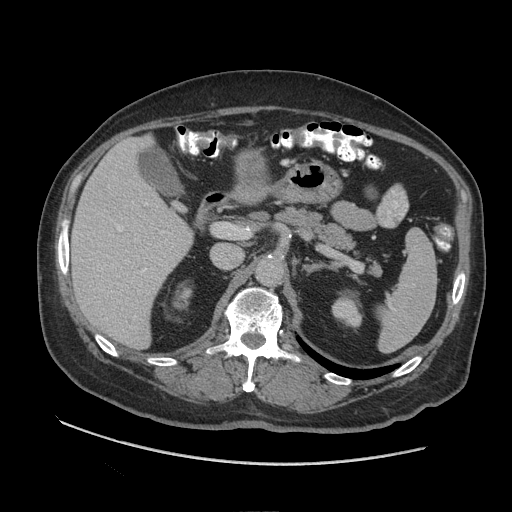
Contrast-enhanced abdominal CT (liver protocol), one axial slice. Position 51 of 109 along the scan axis. Reconstruction kernel STANDARD. 140 kVp. Soft-tissue window (W 400 / L 40 HU). 2.5 mm slice thickness. 512 × 512 image matrix, field of view 420 × 420 mm. From the clinical record (not read from this slice): diagnosis: hepatocellular carcinoma (patient treated with transarterial chemoembolisation; whether this scan precedes or follows treatment is not stated here); TNM stage (as recorded): Stage-I.
Annotated regions visible in this slice (semi-automatic segmentation, software-assisted and operator-edited):
- liver parenchyma outside the tumour (the mass and vessels are separate outlines, so this box may not span the whole liver): bounding box [x1, y1, x2, y2] px = [68, 136, 192, 348]
- mass: [238, 159, 265, 188]
- liver vessels: [117, 202, 164, 273]